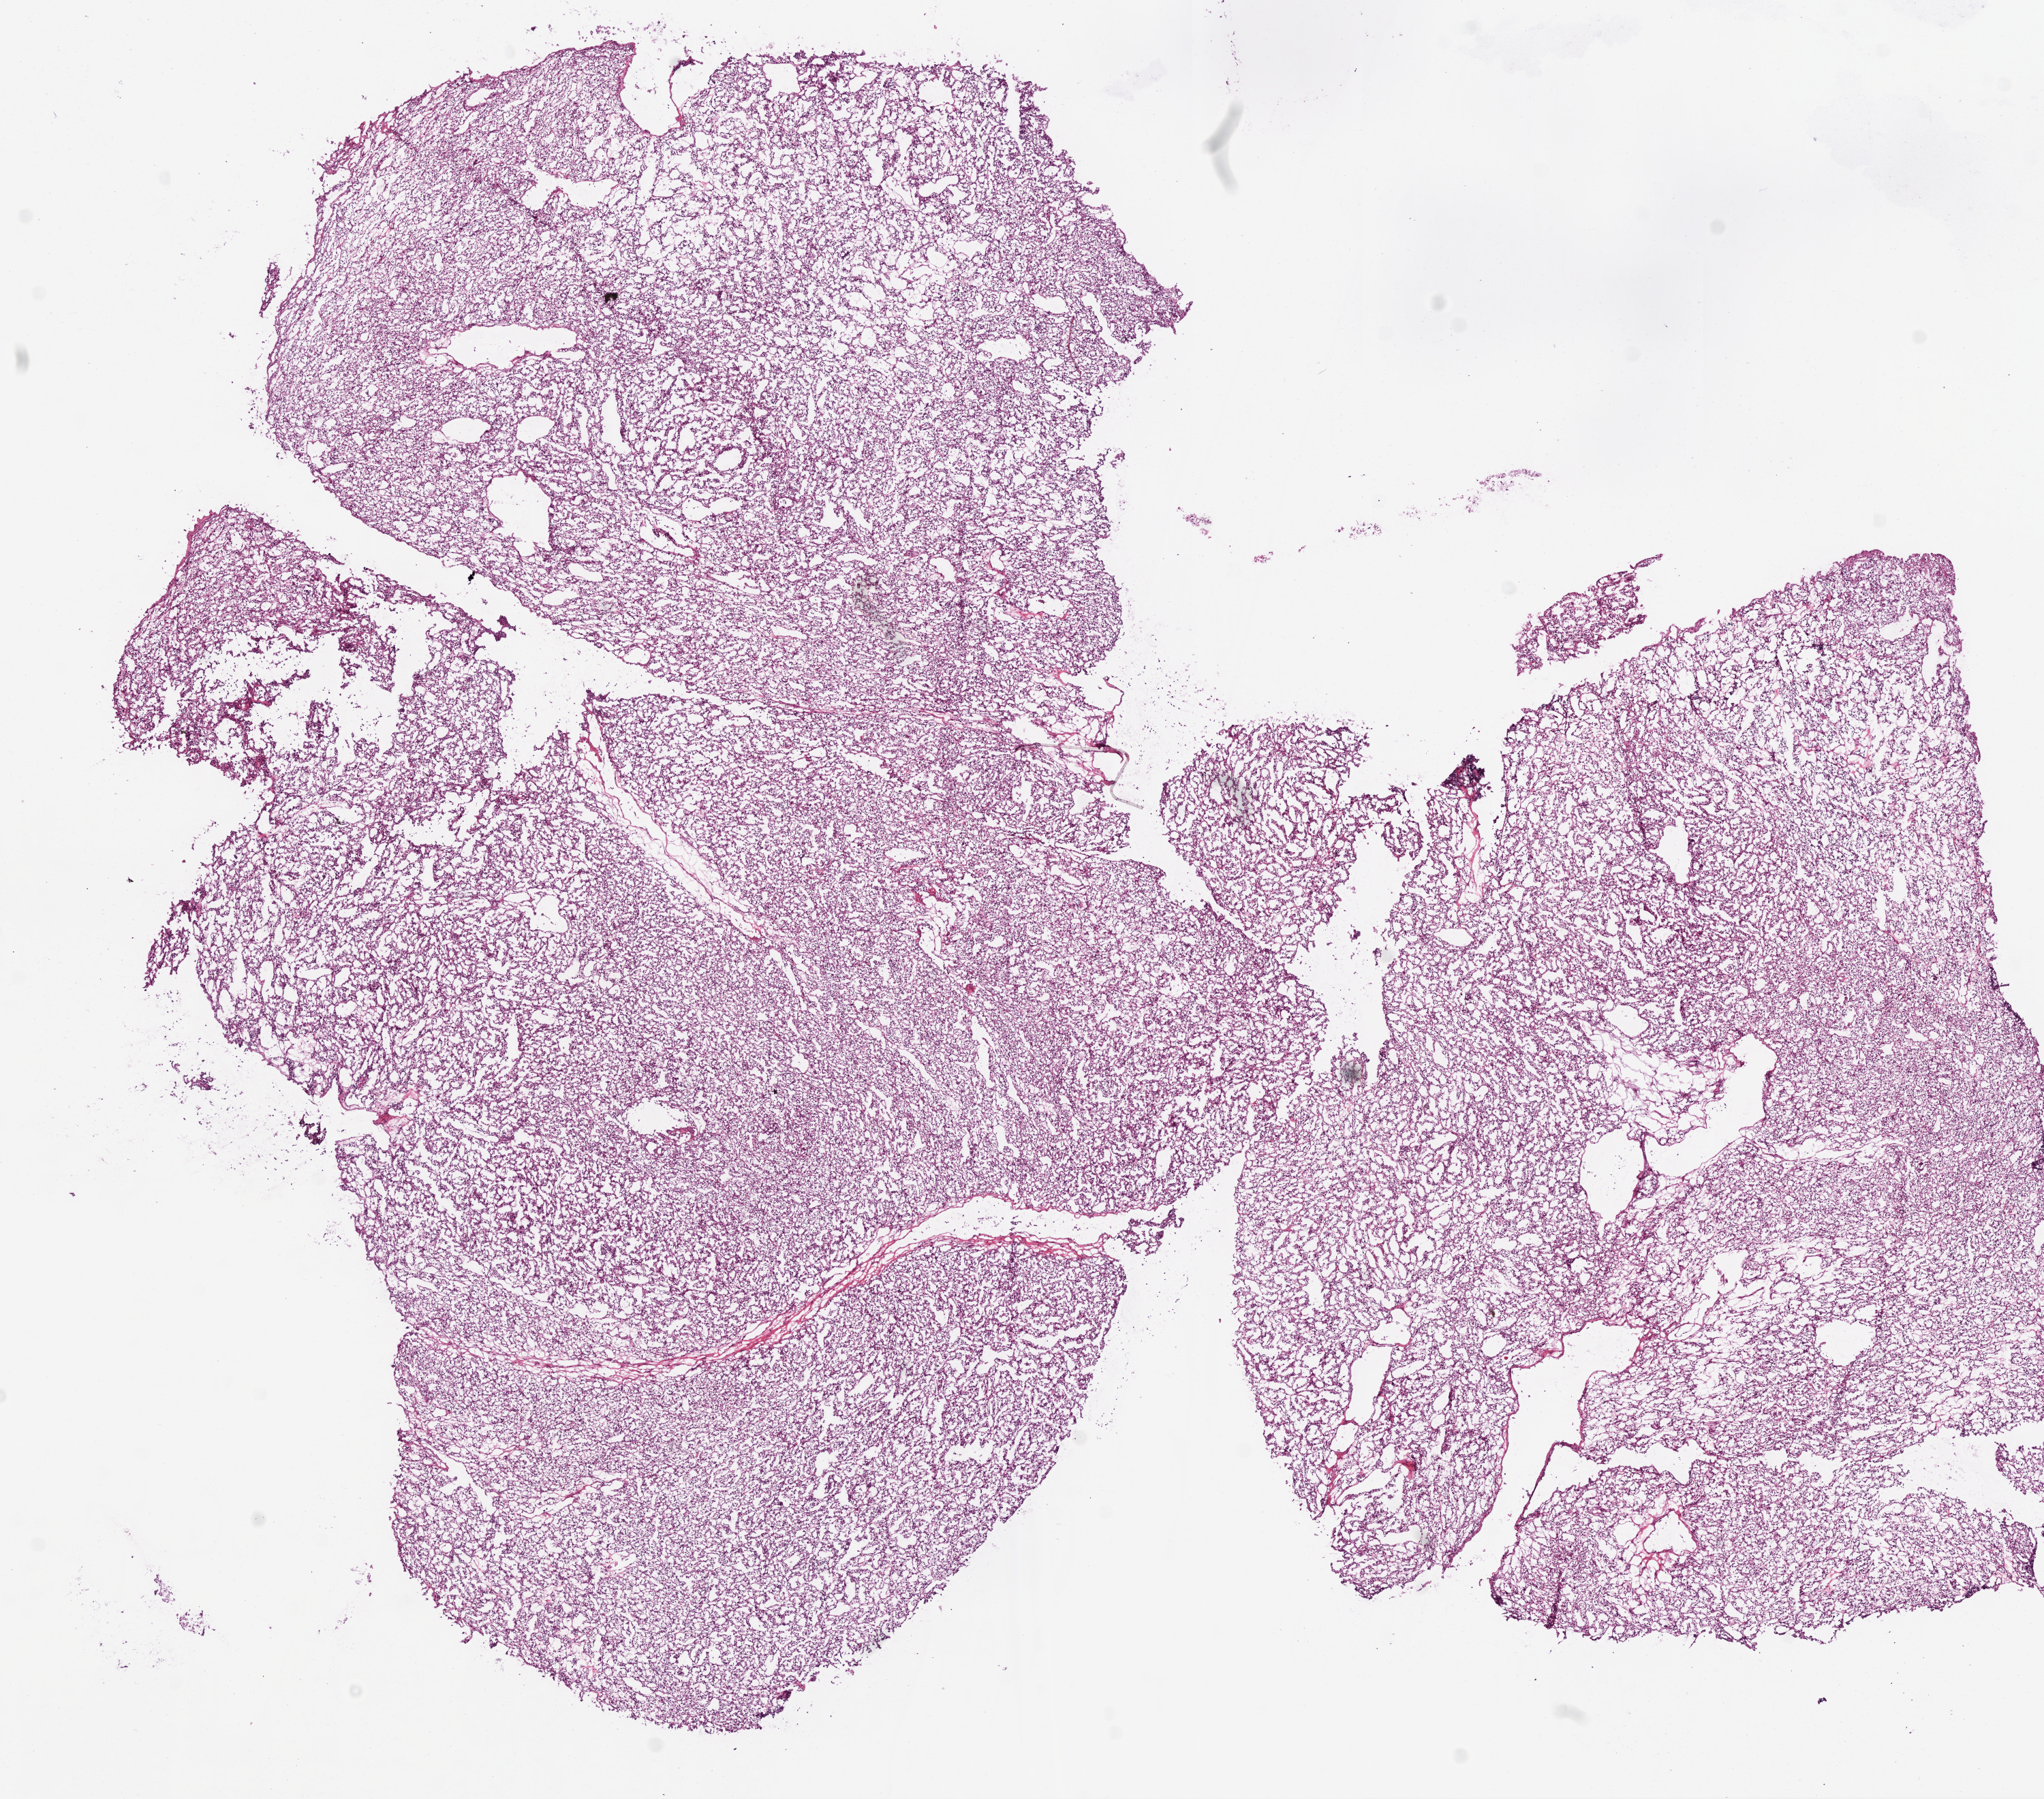
Whole-slide histology image, H&E-stained, a low-resolution overview of the entire scanned area, about 12.0 x 10.6 mm; frozen section from the bottom of the tissue portion; kidney, primary tumour sample. Female, age 64 years at initial diagnosis. Histologic grade: G1 (well differentiated). Slide review estimates, as recorded: tumour cells 95%, tumour nuclei 90%, normal cells 0%, stromal cells 5%, necrosis 0%.
• laterality: right
• diagnosis: Clear cell adenocarcinoma, NOS
• AJCC pathologic stage: I